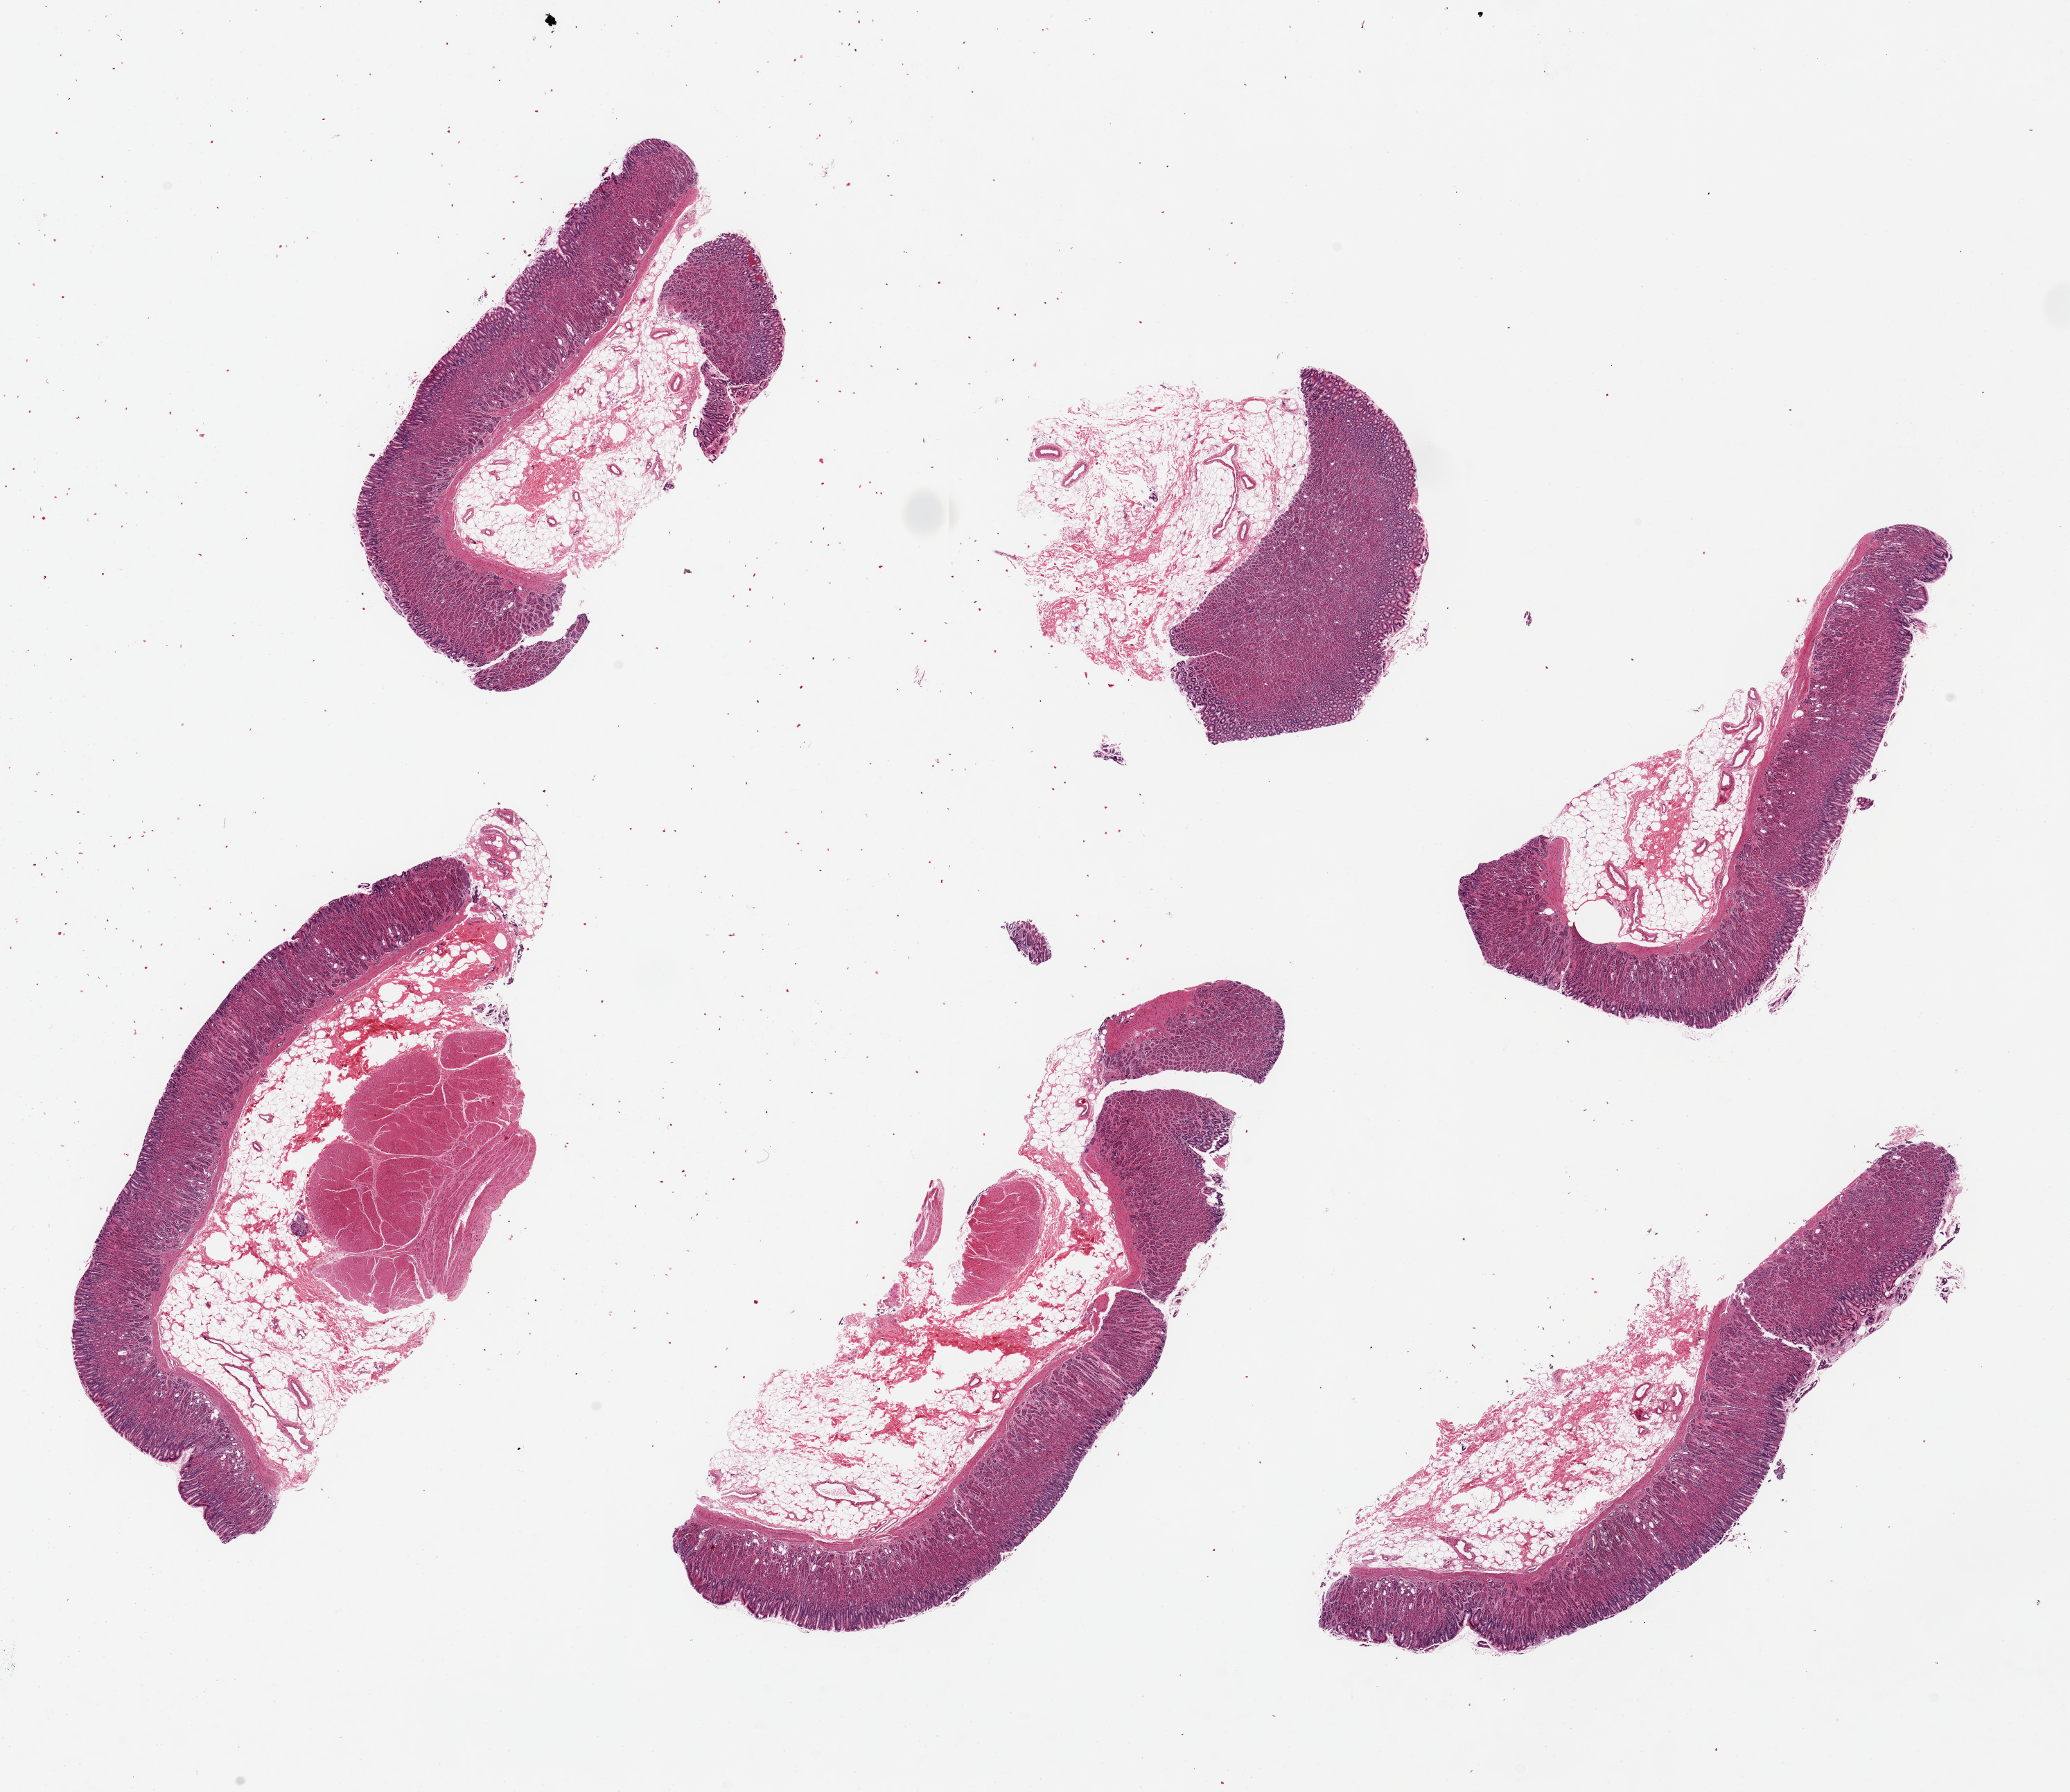
Digitized H&E-stained section, whole scanned area (about 23.6 x 20.5 mm) shown as a low-resolution overview. PAXgene-fixed paraffin-embedded (PFPE) section. Sampled site (target tissue): stomach. Donor tissue sample.
Pathologist's review note for this sample: 6 pieces ~7x2mmm. Mucosa well-preserved, 20-50% of thickness.